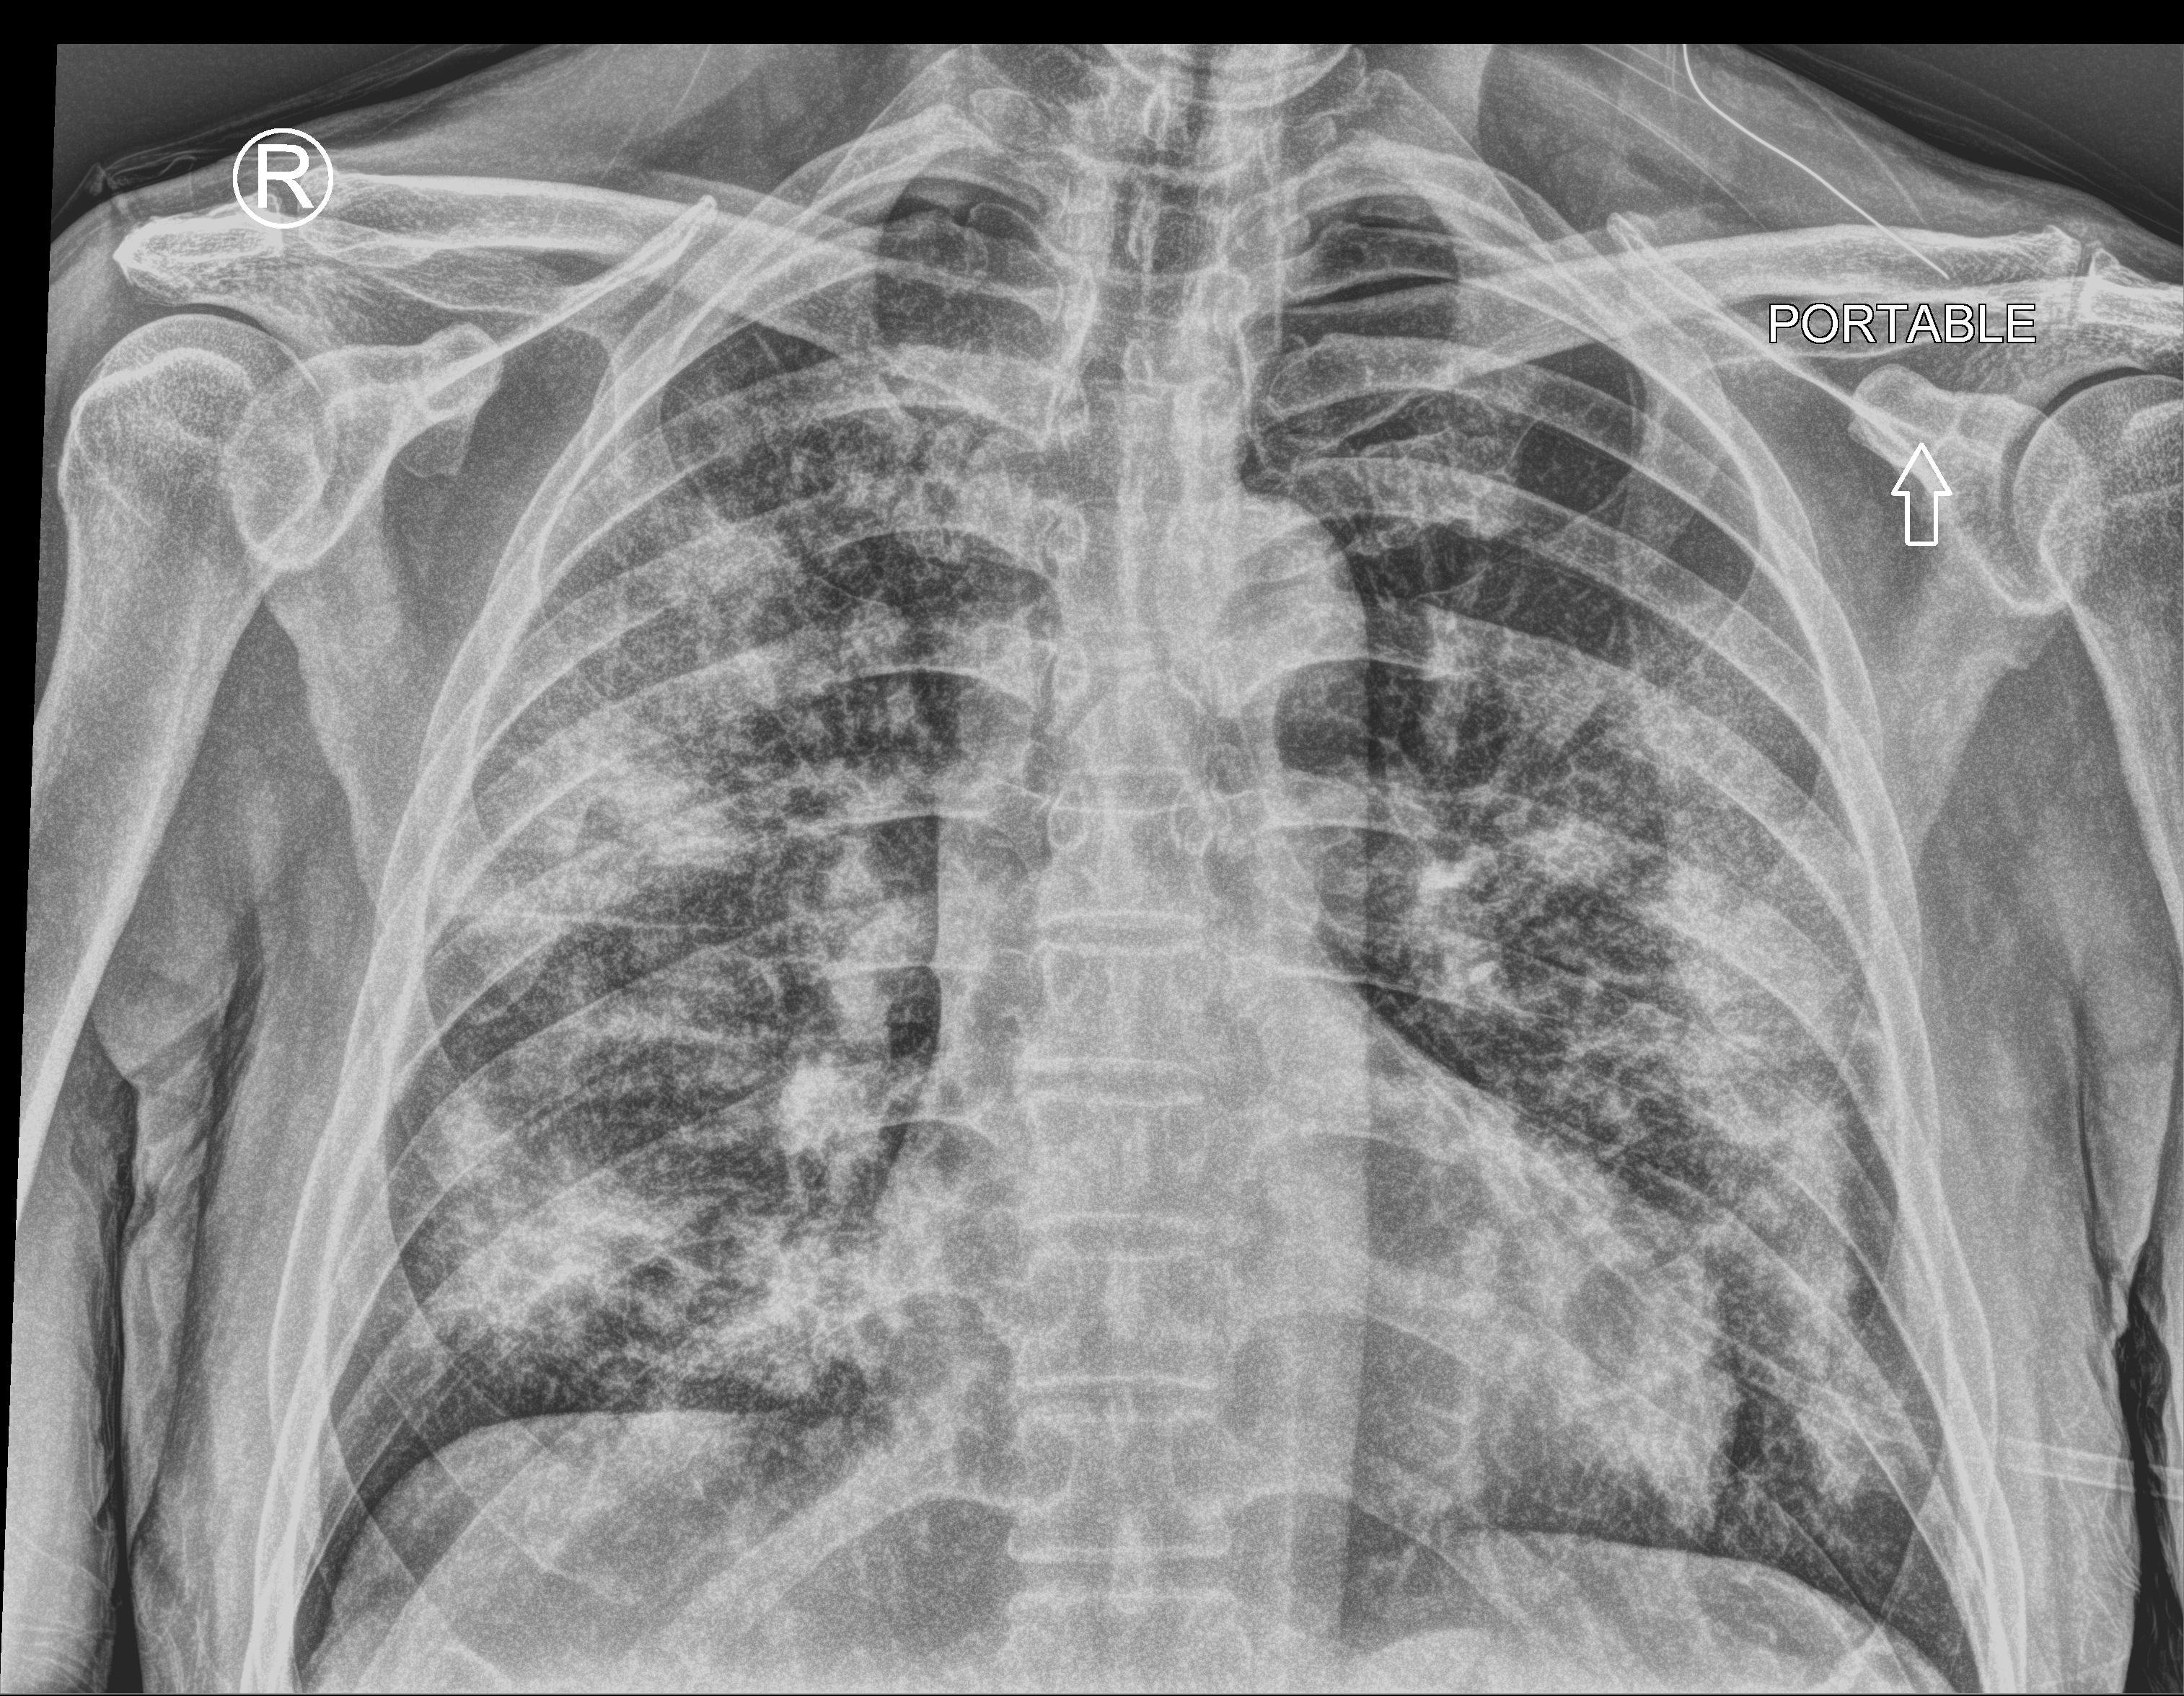
Bedside chest radiograph (computed radiography), anteroposterior (AP) projection. Male patient hospitalised with COVID-19, age 60–74 years.
From the hospital-stay record, not from the radiograph (when in the stay this image was taken is not recorded):
- length of hospital stay: 5 days